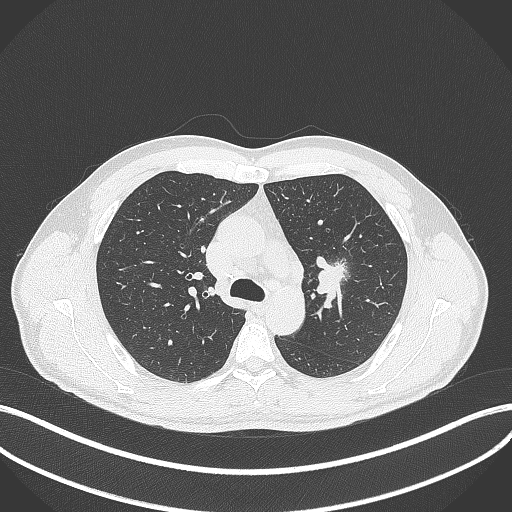
Chest CT, one axial slice; slice 287 of 392 in the series (ordered by position); reconstruction kernel B70f; lung window (W 1500 / L -600 HU); 1 mm slice thickness; 512 × 512 image matrix, field of view 400 × 400 mm. Patient: male, 50 years. Case-level facts recorded for this patient, not image findings: clinical TNM (as recorded): T1c N1 M1b.
Annotated regions visible in this slice (bounding box drawn by a radiologist):
- lung tumour (recorded histology: squamous cell carcinoma): box from (x=313, y=255) to (x=351, y=297) px